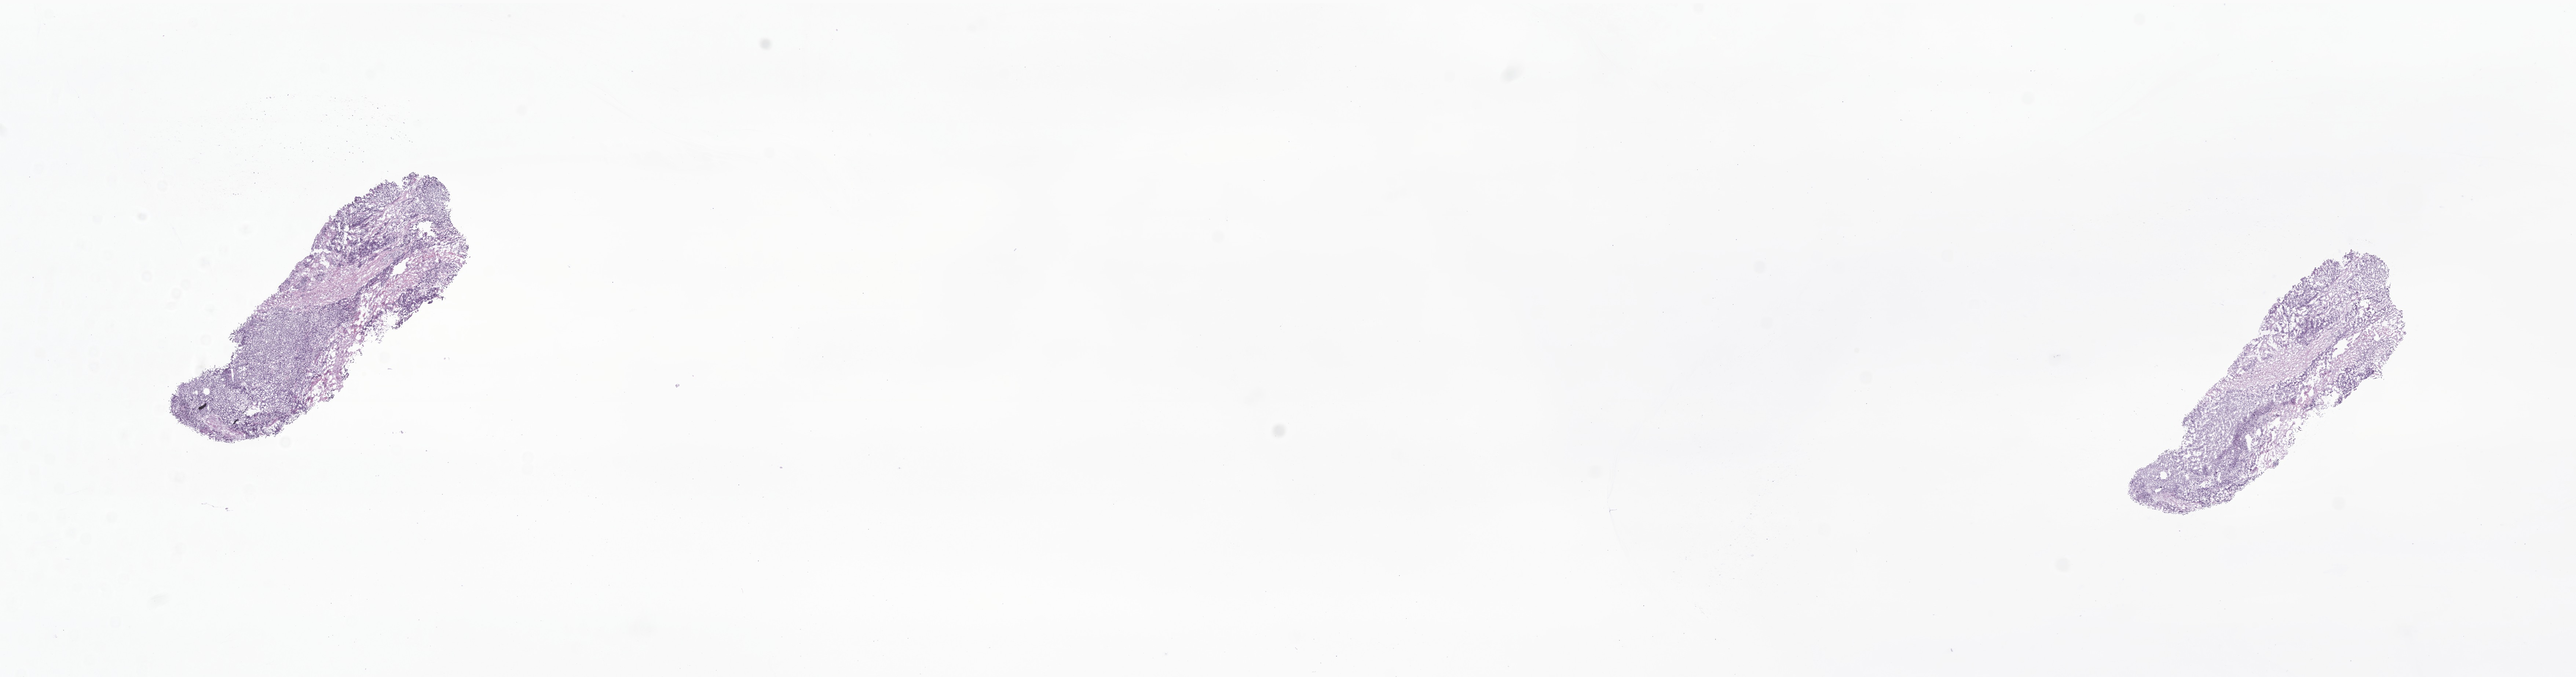
Hematoxylin and eosin (H&E) whole-slide image of tumor tissue from the adrenal gland — whole scanned area (about 29.6 x 7.8 mm) shown as a low-resolution overview. Cryosection (OCT / tissue freezing medium). Male patient, age 827 days (about 2.3 years).
Diagnosis: Neuroblastoma, NOS.